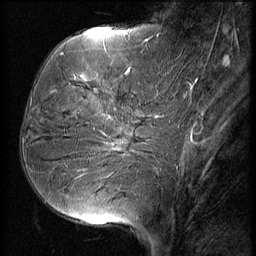
Breast MRI (dynamic contrast-enhanced), one sagittal slice. Position 19 of 56 along the scan axis. 3 images stored at this slice position (order not interpretable as contrast timing). 1.5 T. TE 4.2 ms, TR 9 ms. 2.5 mm slice thickness. 256 × 256 image matrix, field of view 180 × 180 mm. Female patient, age 51 years. Case-level facts recorded for this patient, not image findings: setting: breast cancer imaged before/during neoadjuvant chemotherapy; receptor status: HR-positive, HER2-negative.
Structures marked on this image (semi-automatic segmentation, software-assisted and operator-edited):
- analysis volume of interest (the breast-tissue region the enhancement analysis was run in; not a lesion): bounding box (x1, y1, x2, y2) in pixels: (23, 56, 156, 165)
- tumour enhancement mask (voxels above the 140 % enhancement threshold inside the analysis volume of interest): (113, 70, 129, 145)